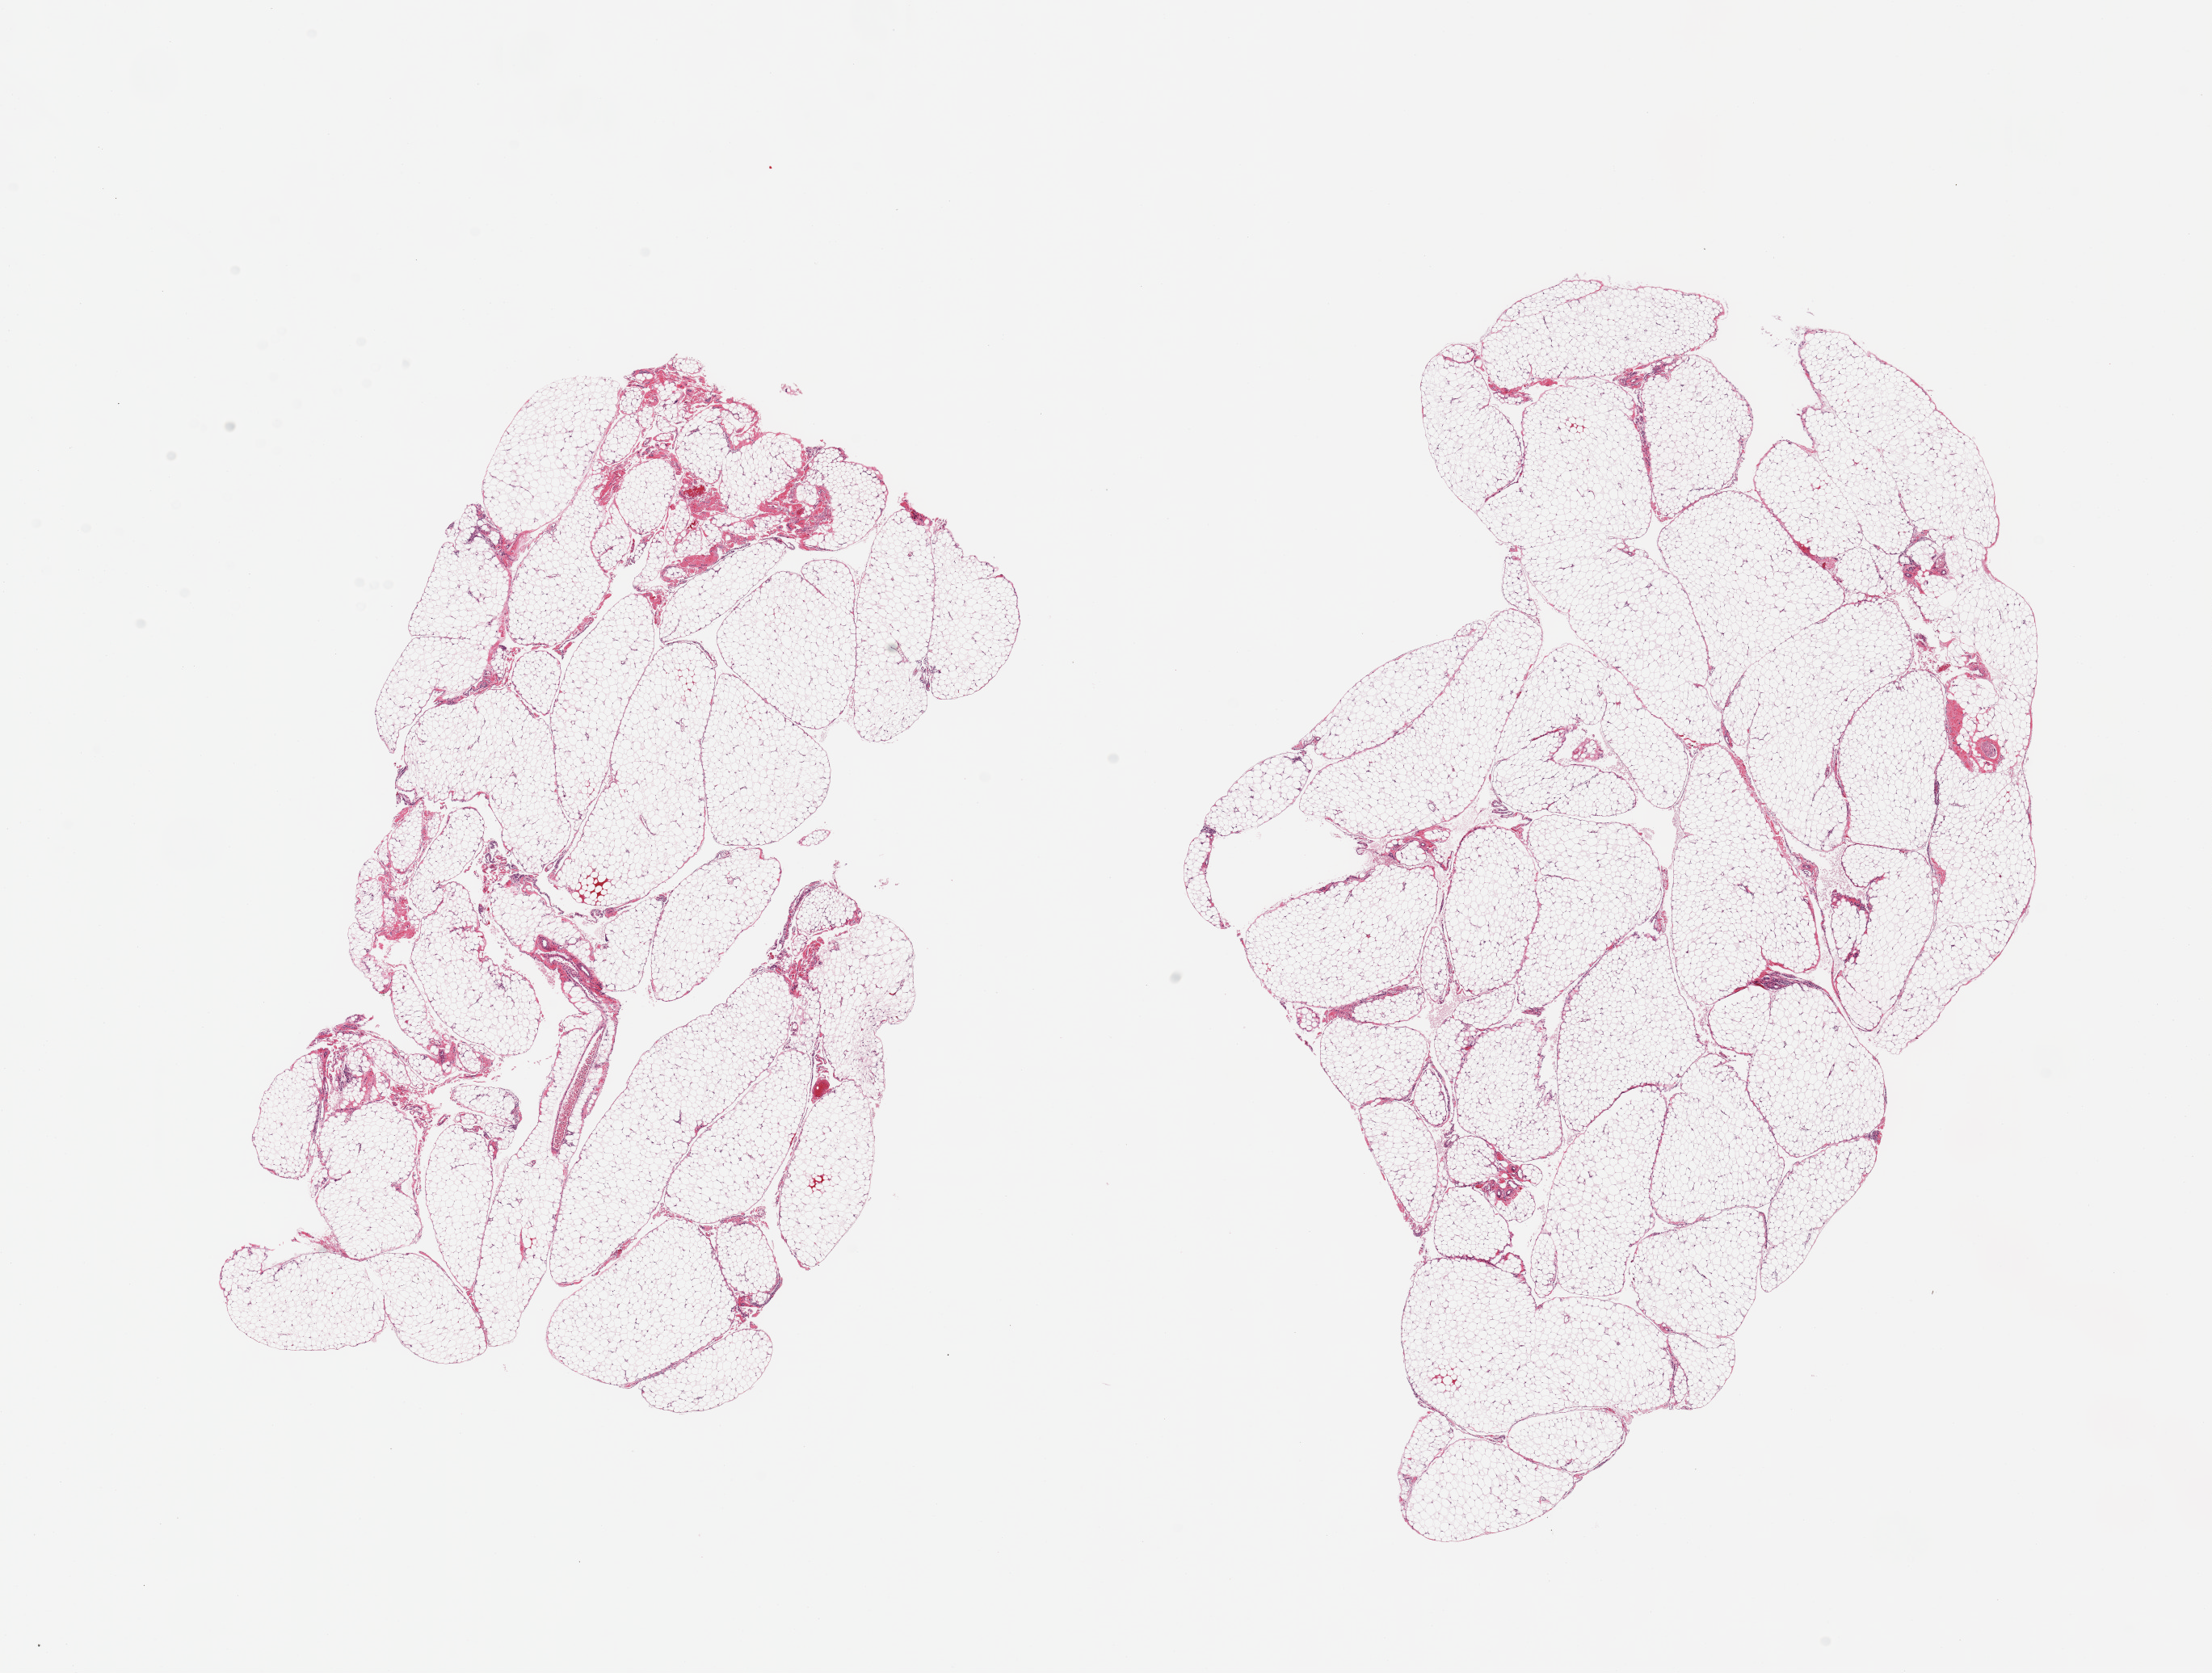
Whole-slide image, hematoxylin and eosin (H&E) stain — whole scanned area (about 21.7 x 16.4 mm) shown as a low-resolution overview, PAXgene-fixed paraffin-embedded (PFPE) section, sampled site (target tissue): omentum, tissue donor sample.
Review note (as recorded): 2 pieces, minimal interstitial fascia.